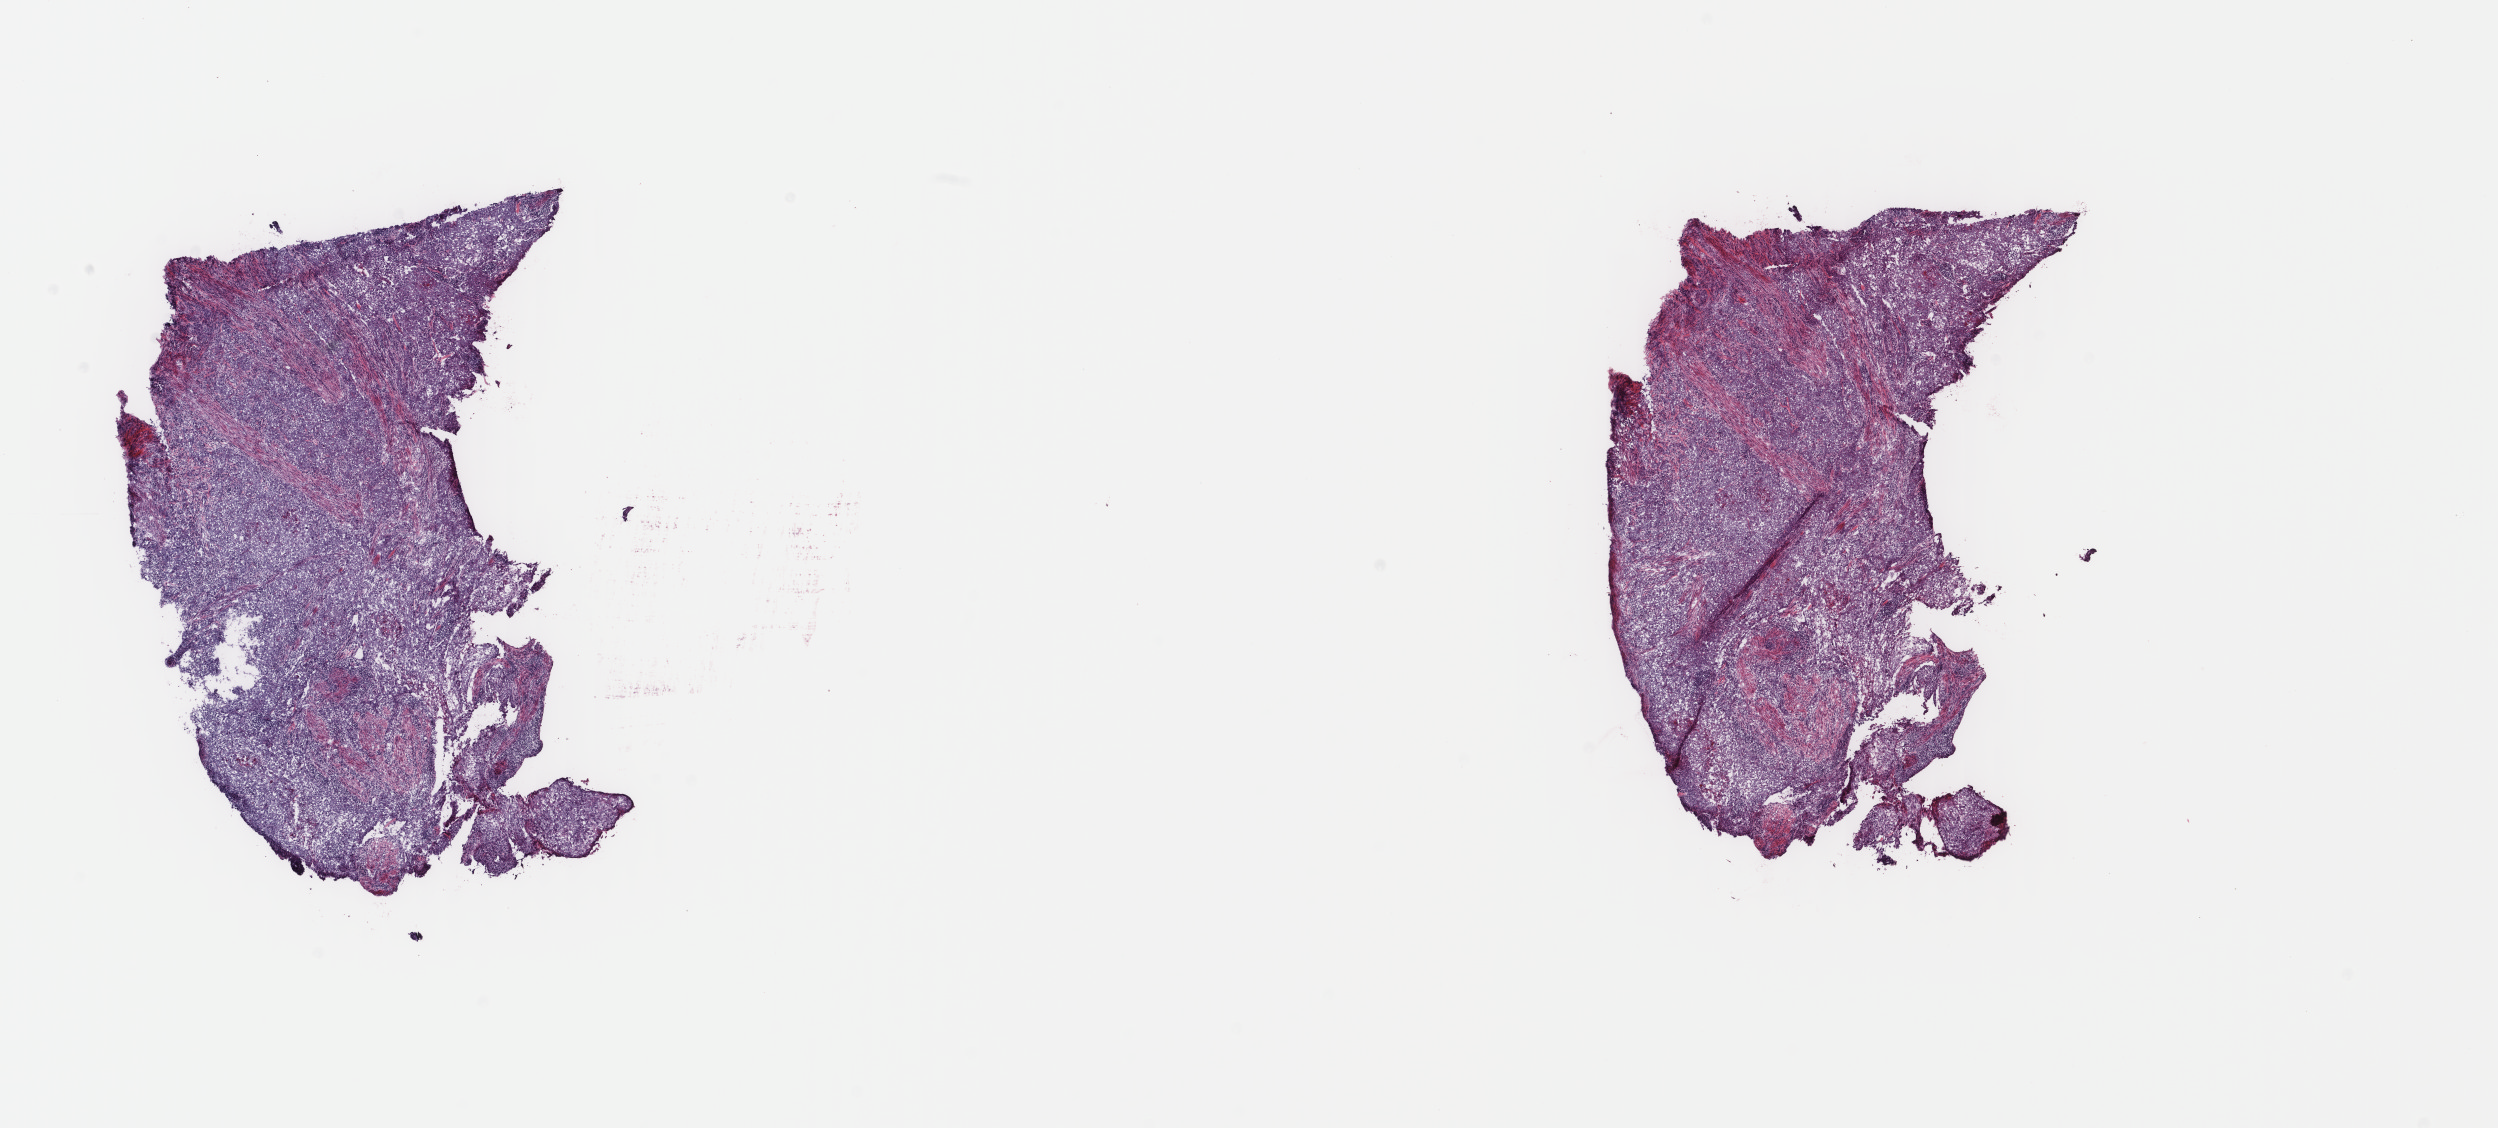
Hematoxylin and eosin (H&E) stained whole-slide image — low-resolution overview of the scanned area, about 19.8 x 9.0 mm (slide scanned at 40x); frozen section from the top of the tissue portion; bladder, primary tumour sample. Female patient; age at initial diagnosis 74 years. Slide review estimates, as recorded: tumour cells 85%, tumour nuclei 75%.
Histologic diagnosis: Papillary transitional cell carcinoma.